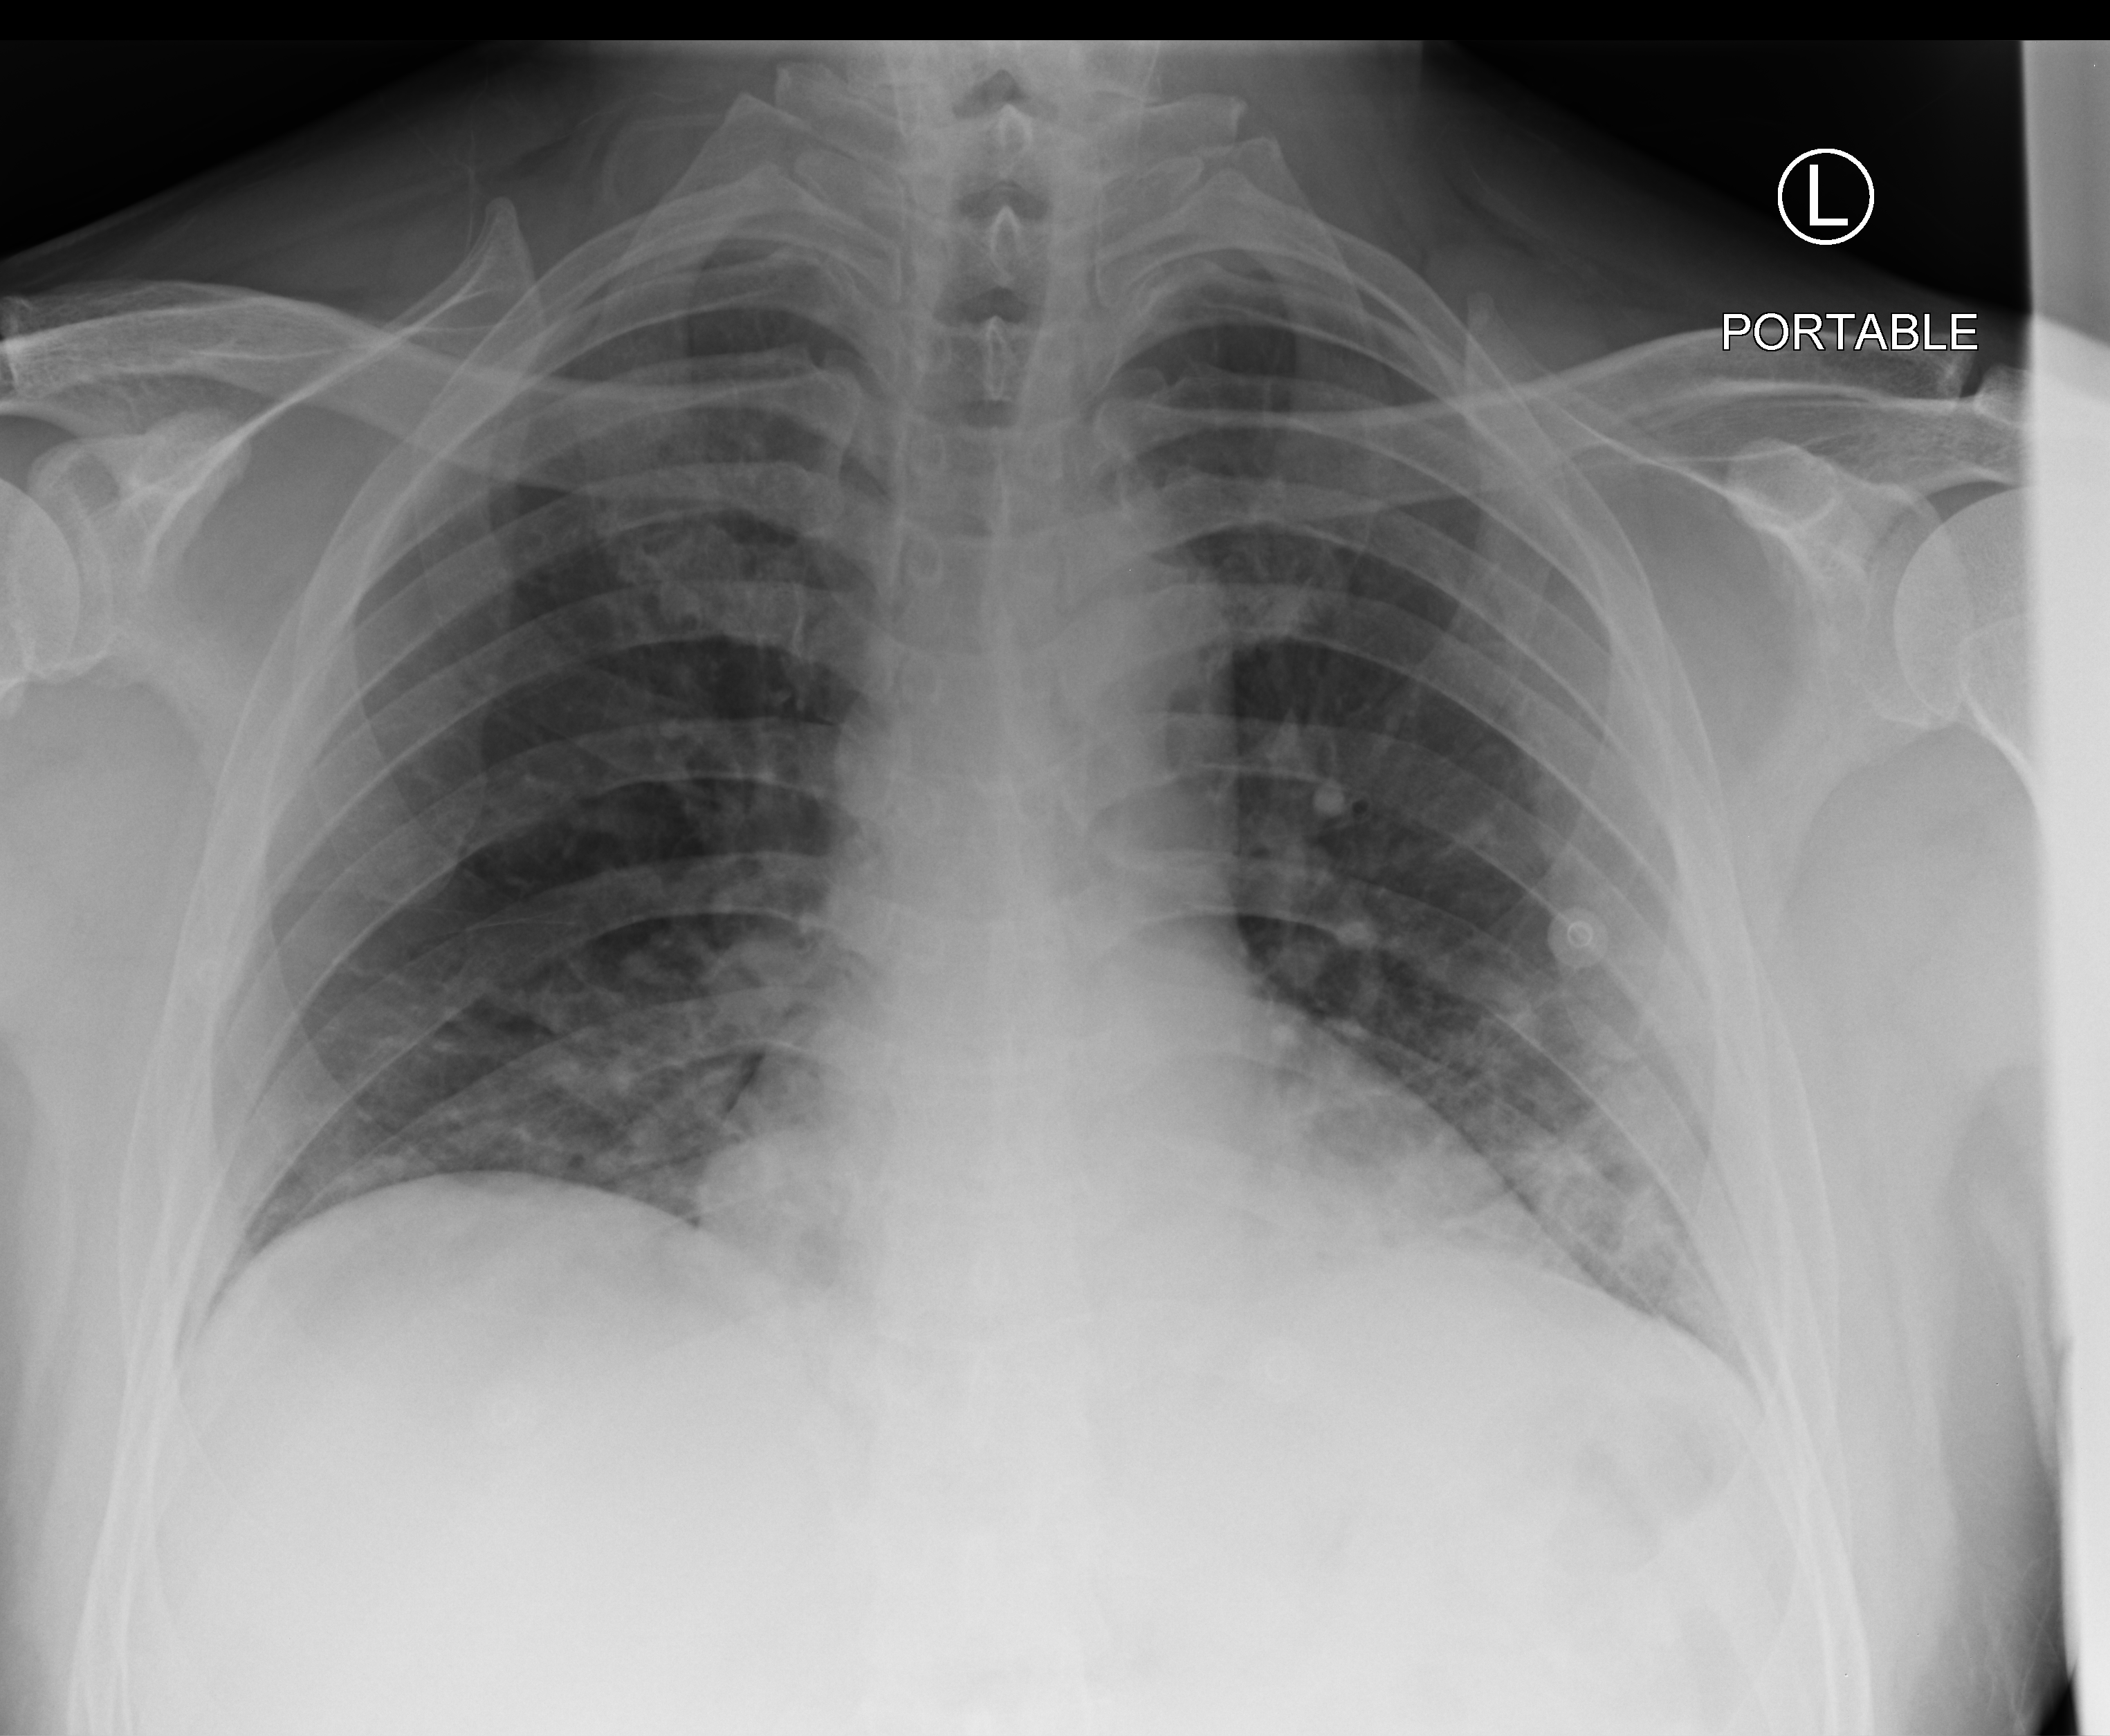
Chest X-ray (portable), anteroposterior (AP) projection. Patient hospitalised with COVID-19; male, aged 18–59 years.
From the hospital-stay record, not from the radiograph (when in the stay this image was taken is not recorded):
- hypertension (admission record): no
- admitted to intensive care during this hospital stay: no
- mechanically ventilated during this hospital stay: no